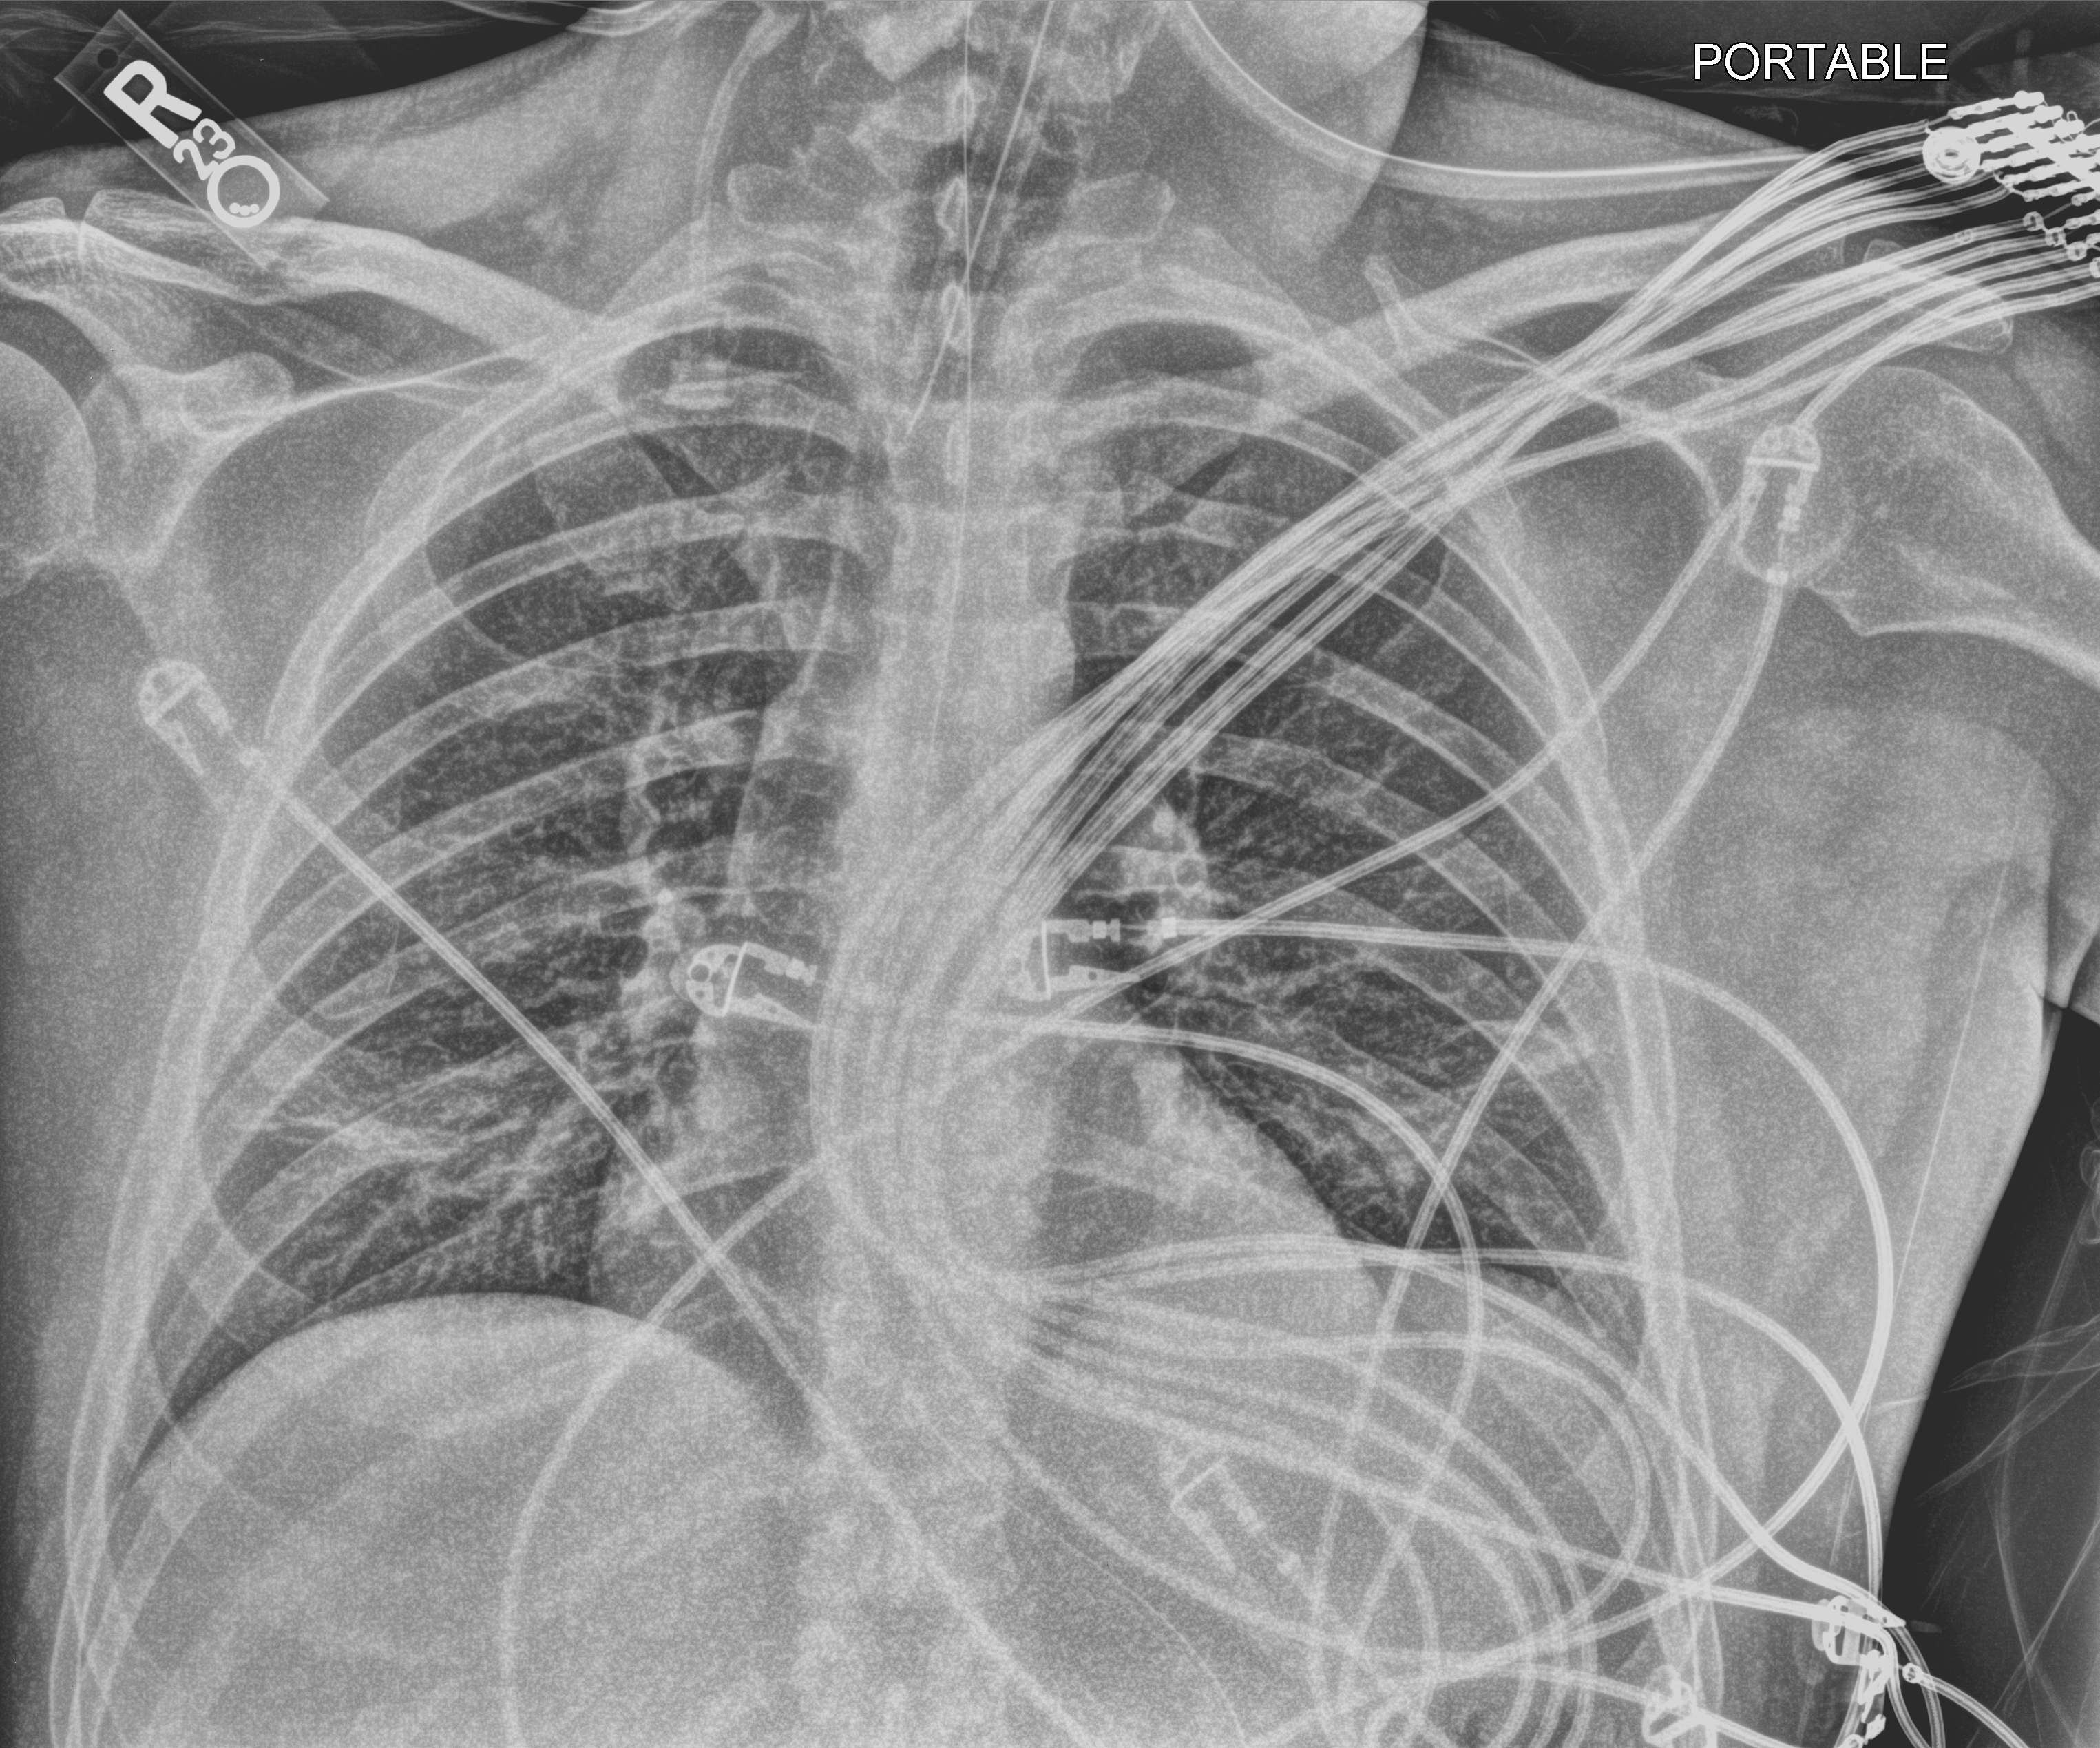
Bedside chest radiograph (computed radiography), anteroposterior (AP) projection. Patient hospitalised with COVID-19; male, aged 18–59 years.
Hospital-stay facts (about this admission, not read from this image; timing relative to this image not recorded):
- mechanically ventilated during this hospital stay: yes
- admitted to intensive care during this hospital stay: yes